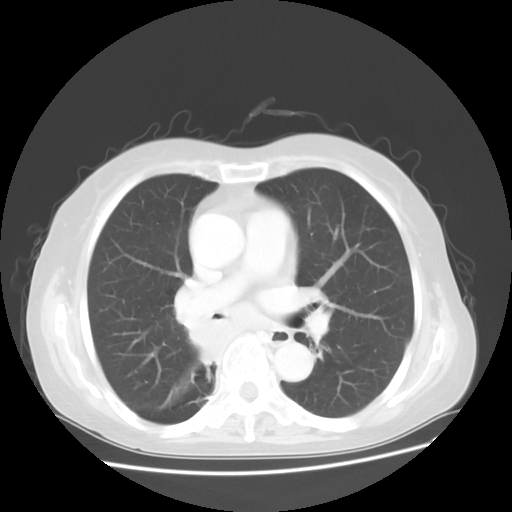
Chest CT, one axial slice; slice 26 of 48 in the series (ordered by position); reconstruction kernel STANDARD; lung window (W 1500 / L -600 HU); 5 mm slice thickness; 512 × 512 image matrix, field of view 360 × 360 mm. Female patient, age 63 years. From the clinical record (not read from this slice): clinical TNM (as recorded): T2 N3 M1b; histopathological grade: G3.
Annotated regions visible in this slice (bounding box drawn by a radiologist):
- lung tumour (recorded histology: small cell carcinoma): box from (x=188, y=317) to (x=226, y=370) px